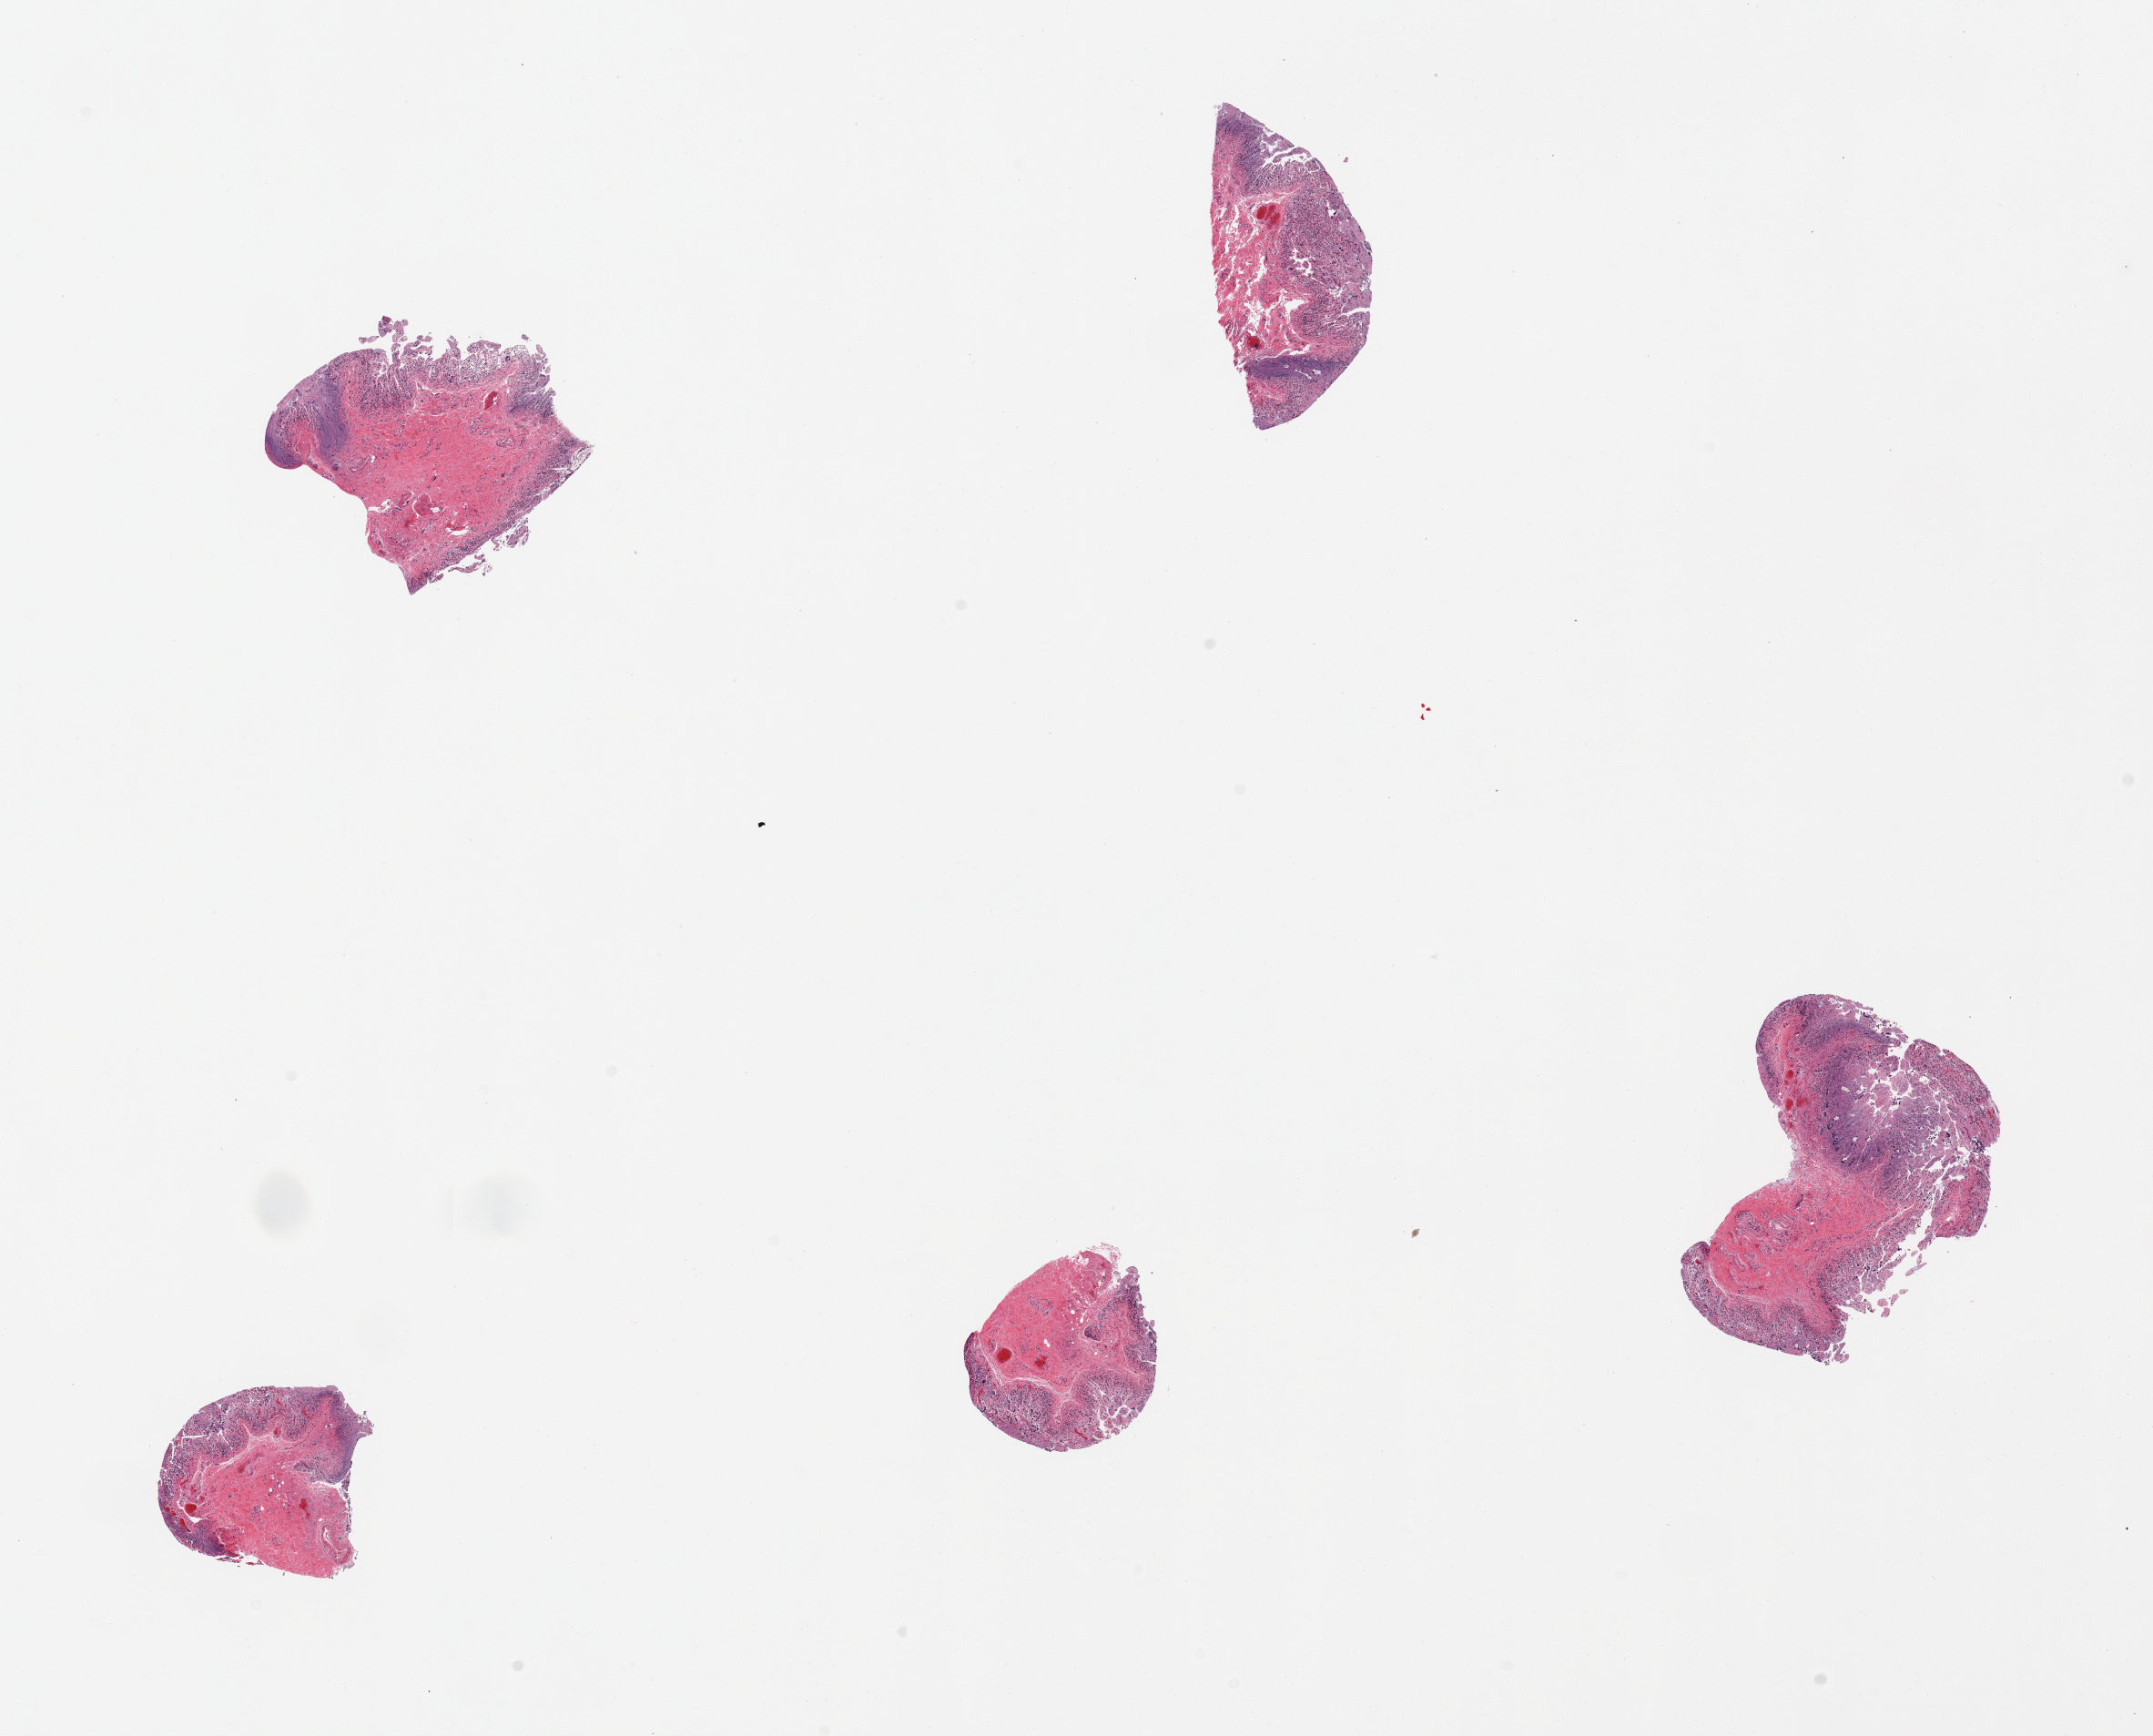
Digitized hematoxylin and eosin (H&E)-stained section — shown as a low-resolution overview of the whole scanned area (about 18.7 x 15.1 mm); PAXgene-fixed, paraffin-embedded tissue; section of ileum (target tissue); donor tissue sample.
- reviewer comment on this tissue sample: 6 pieces, glandular mucosal elements sloughed; residual lymphoid aggregates are ~20%